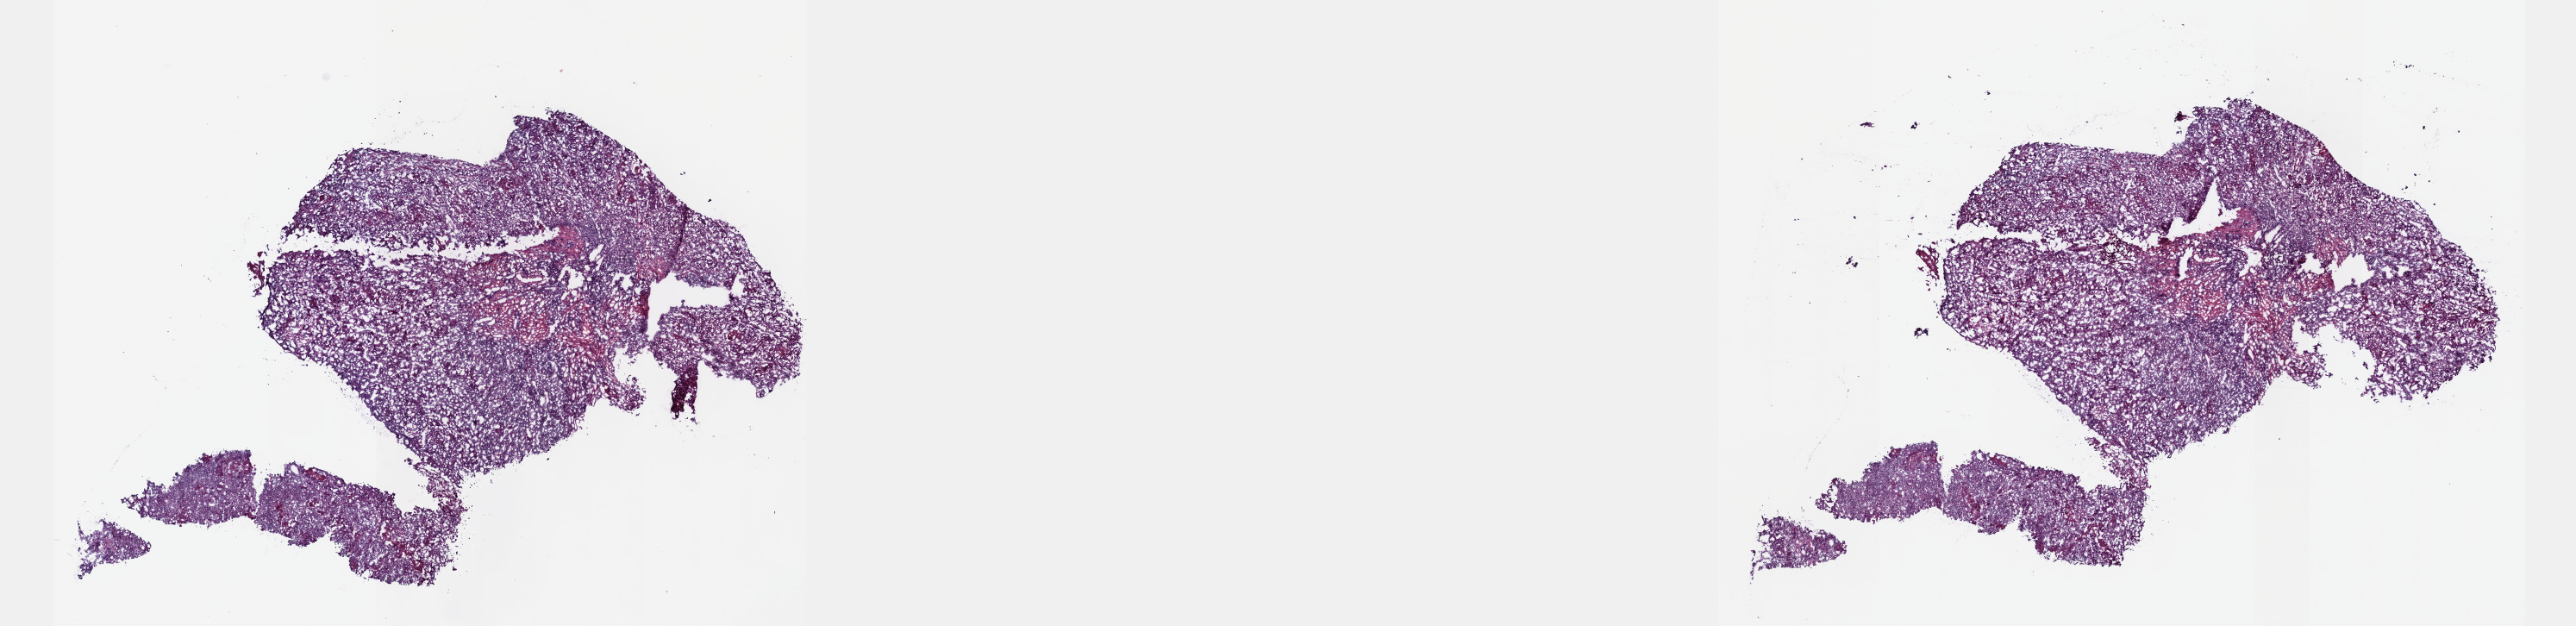
Digitized Hematoxylin and eosin (H&E) stained tissue section (whole slide), low-resolution overview of the scanned area, about 24.1 x 5.9 mm (acquisition: 40x scan), frozen section from the top of the tissue portion, primary tumour sample from the esophagus. Patient: male, age at initial diagnosis 57 years. Histologic grade: G1 (well differentiated). Composition of this section per pathologist review: tumour cells 70%, tumour nuclei 70%, normal cells 0%, stromal cells 30%, necrosis 0%. Inflammatory infiltration, as recorded: lymphocyte infiltration 40%, monocyte infiltration 20%, neutrophil infiltration 20%.
AJCC pathologic stage: IIA (7th edition). Lymph nodes positive (case pathology): 0 of 11 examined. TNM: T3 N0 M0. Histologic diagnosis: Squamous cell carcinoma, NOS (lower third of esophagus).